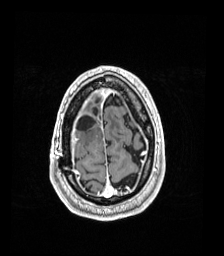
Brain MRI from a brain-tumour surgery series, one axial slice. T1-weighted post-contrast. 1 mm slice thickness. 224 × 256 image matrix, field of view 224 × 256 mm. From the clinical record (not read from this slice): histopathology: Astrocytoma; WHO grade: 4; IDH mutation: yes.
Annotated regions visible in this slice (expert manual segmentation):
- previous resection cavity: box from (x=77, y=114) to (x=95, y=131) px